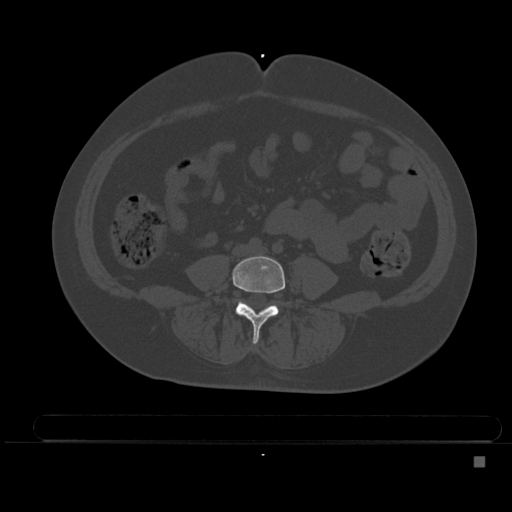
CT including the spine, one axial slice. Position 126 of 495 along the scan axis. Bone window (W 1800 / L 400 HU). 1.5 mm slice thickness. 512 × 512 image matrix. Patient: female, 33 years. Case-level facts recorded for this patient, not image findings: primary cancer: breast.
Annotated regions visible in this slice (semi-automatically segmented with operator editing):
- L4 vertebra: bounding box <233,255,289,344> (left, top, right, bottom; pixels)